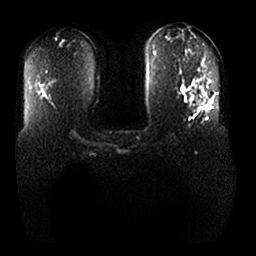
Breast MRI, one axial slice; slice 17 of 25 in the series (ordered by position); diffusion-weighted series; image 2 of 4 stored at this slice position (different b-values; order by instance number); 1.5 T; 4 mm slice thickness; 256 × 256 image matrix. Female patient.
Annotated regions visible in this slice (manually delineated by an expert):
- tumour on diffusion-weighted imaging: bounding box <188,94,211,106> (left, top, right, bottom; pixels)